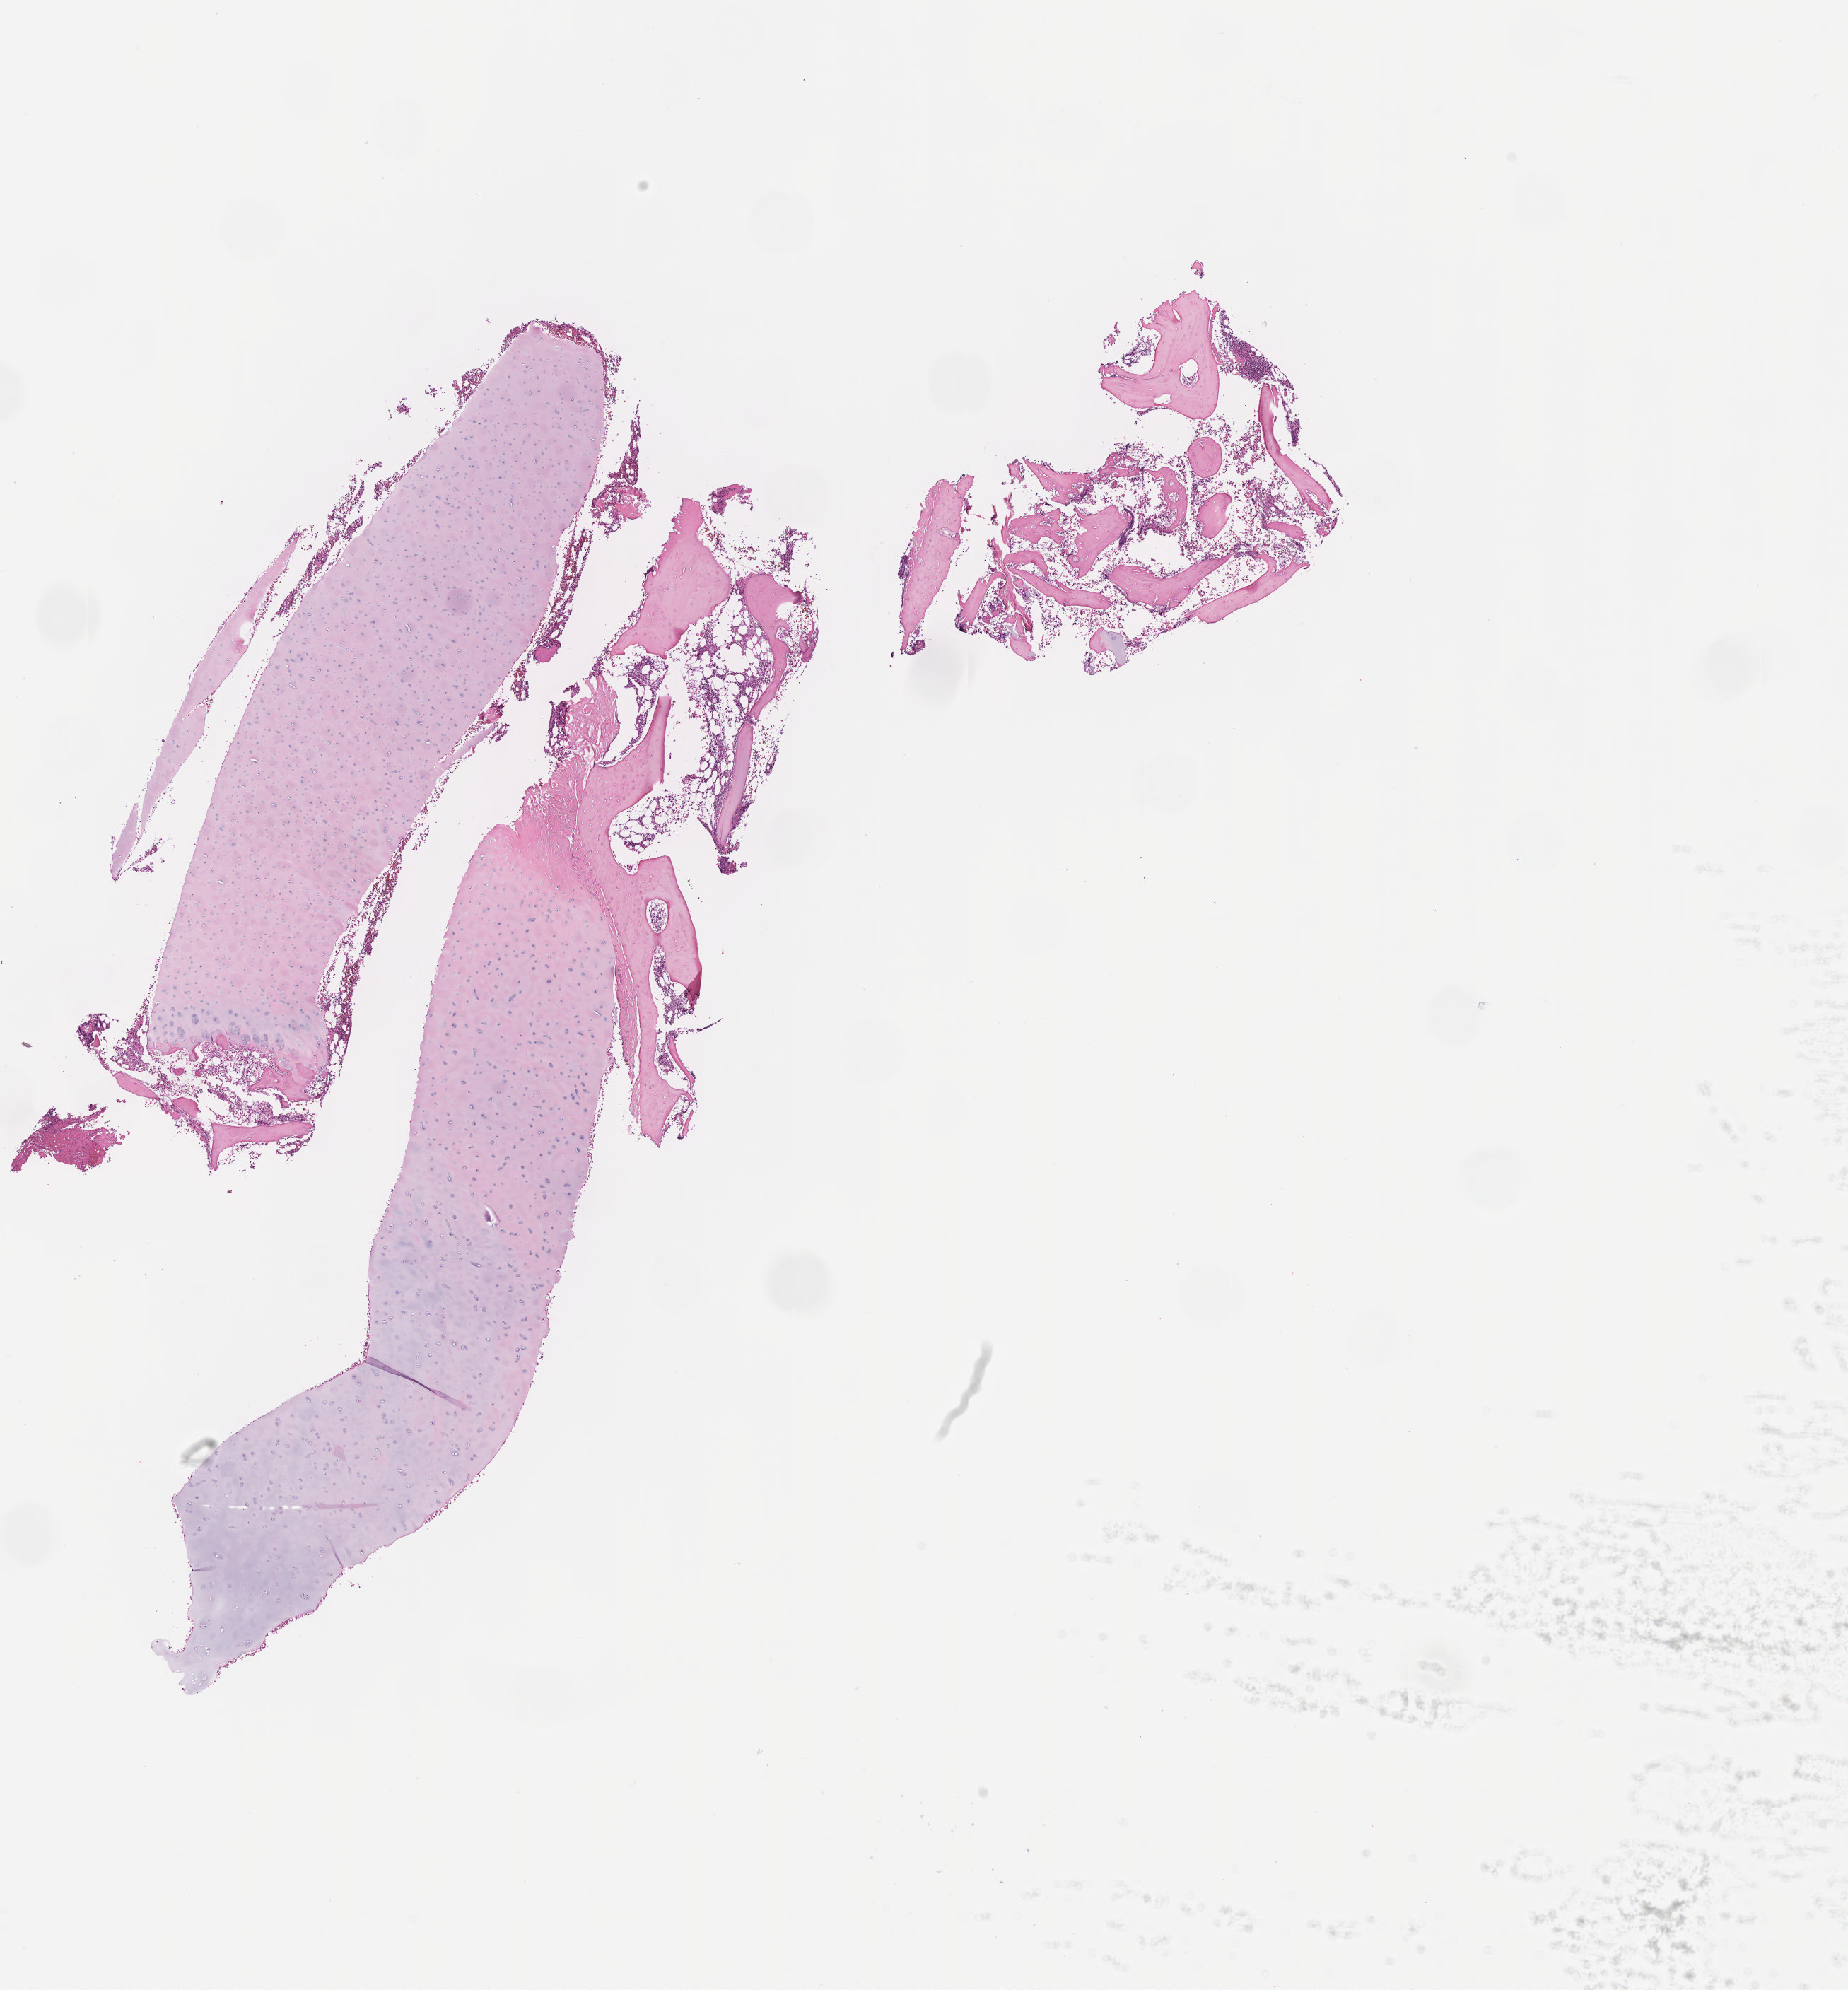
Whole-slide image, hematoxylin and eosin (H&E) stain — a low-resolution overview of the entire scanned area, about 10.6 x 11.4 mm, tumor tissue, site: bone marrow. Patient: female, aged 11.
Diagnosis: Burkitt lymphoma, NOS.